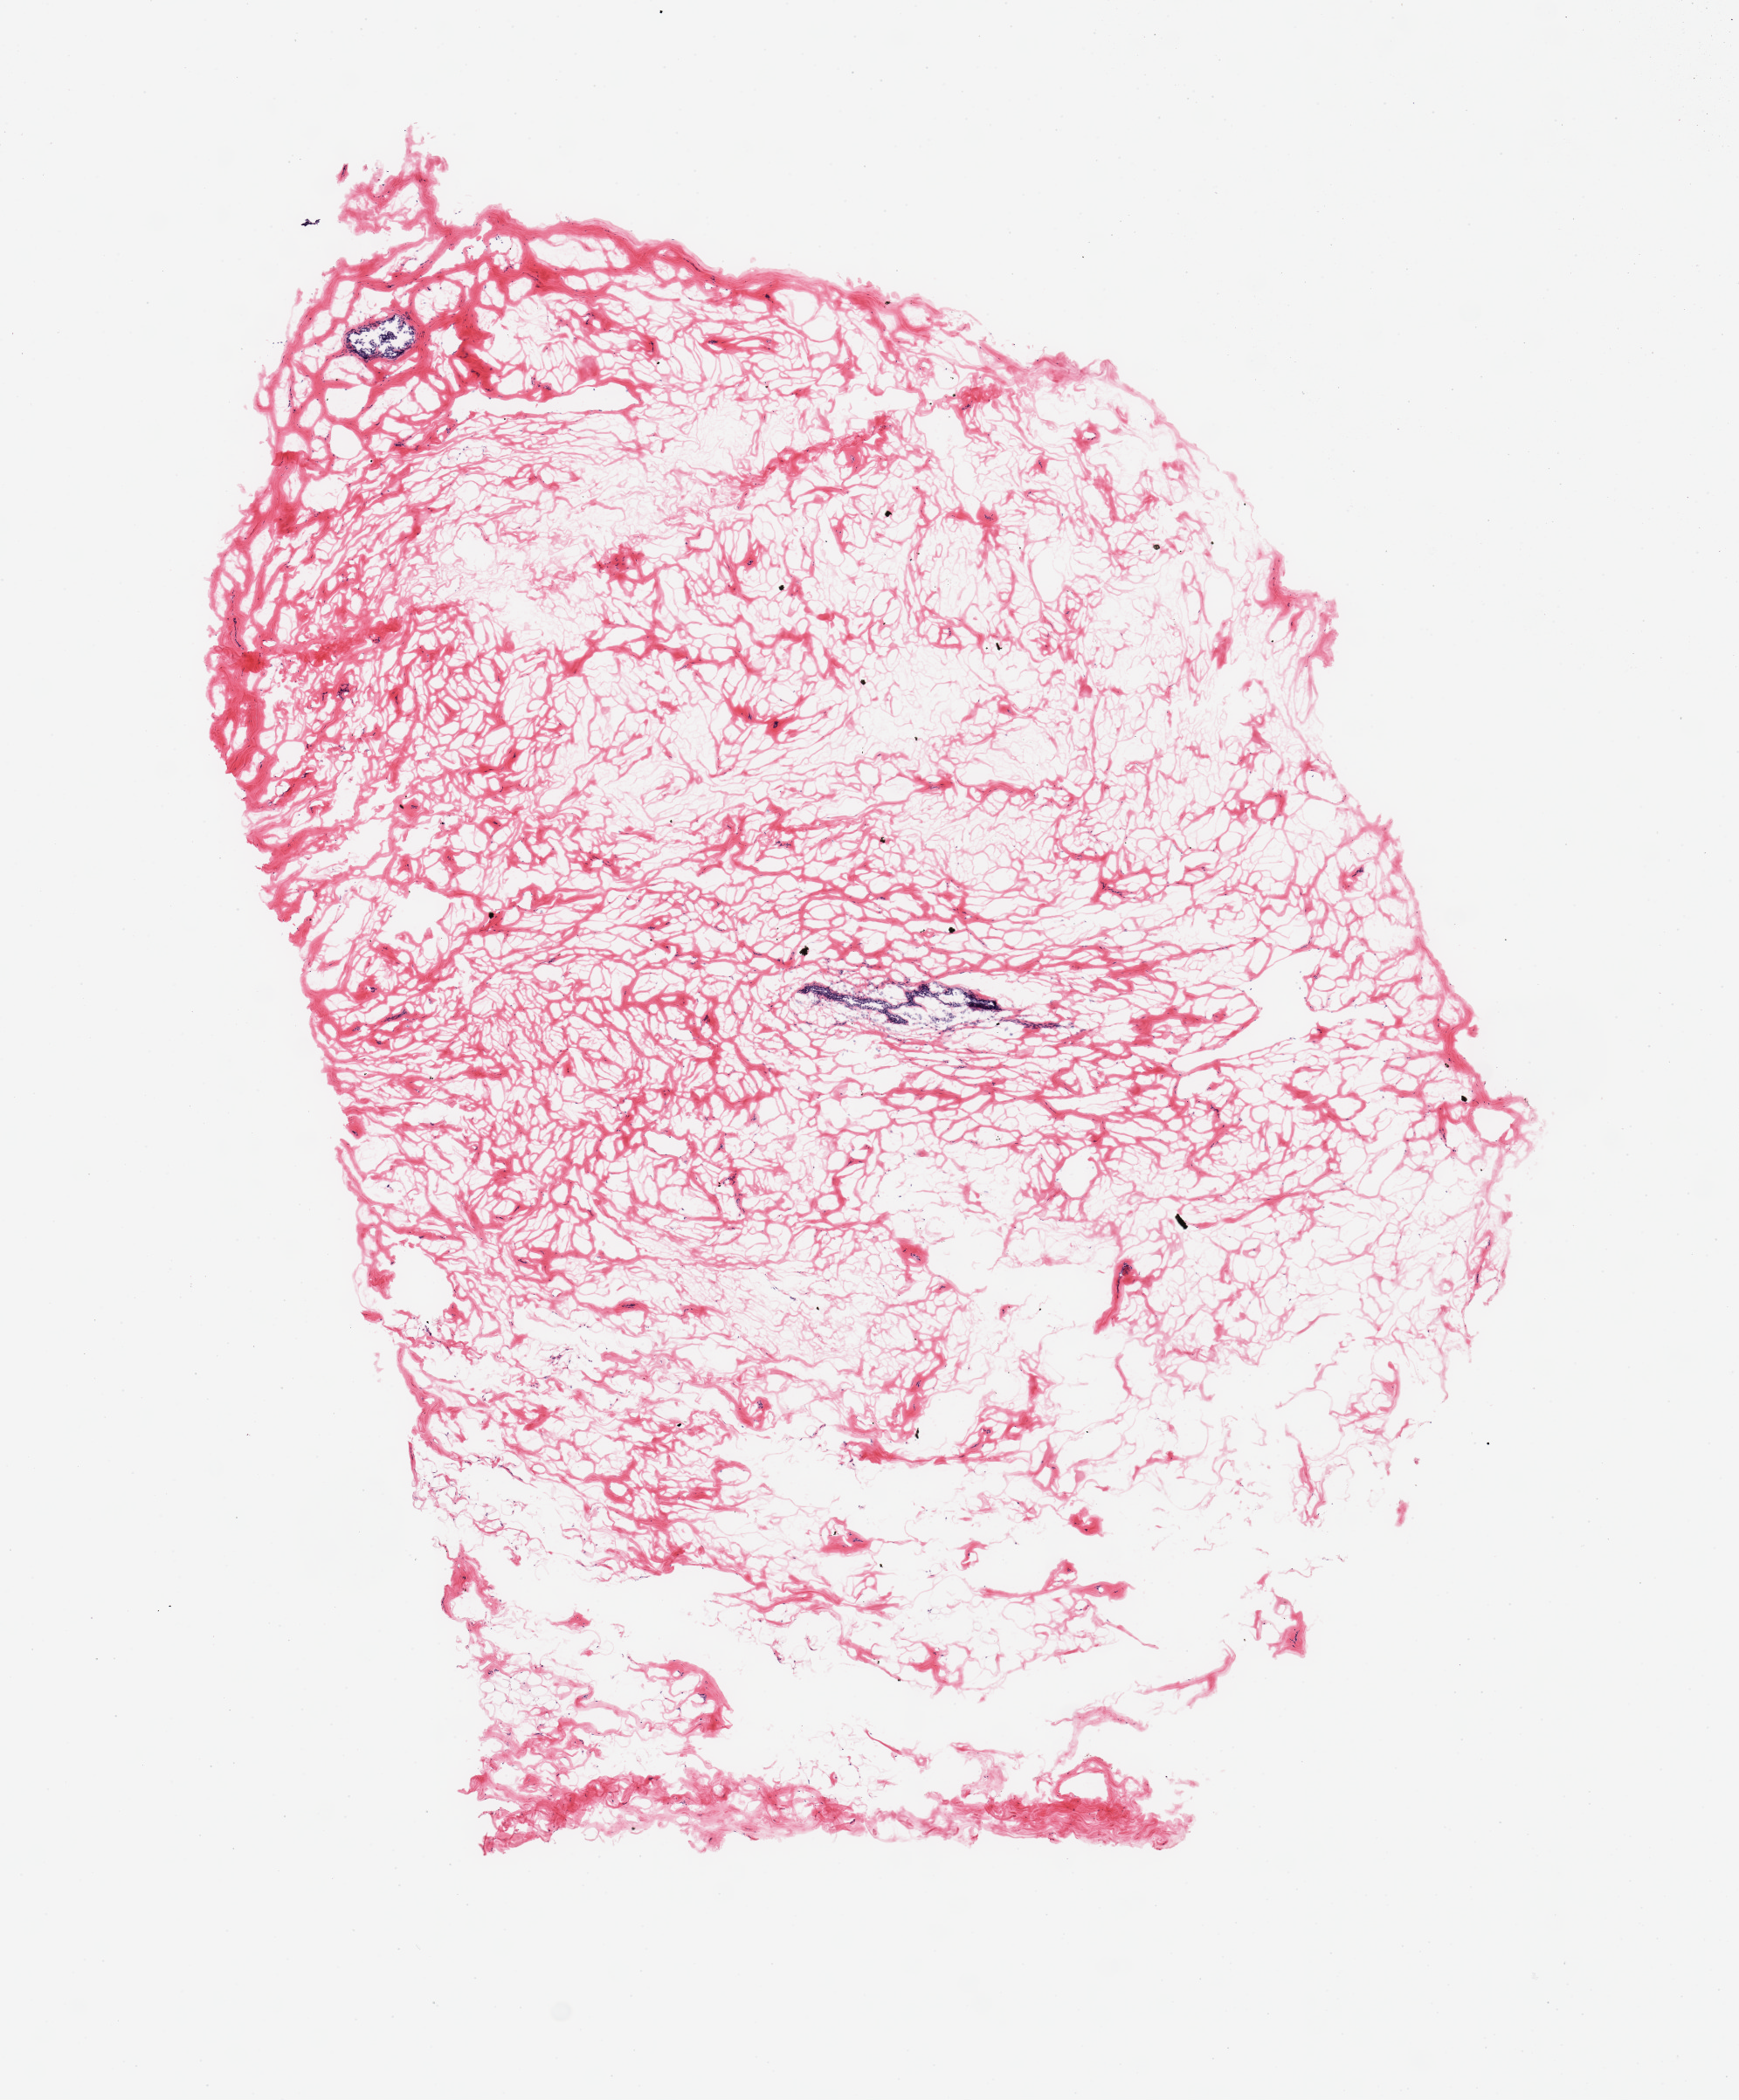
Hematoxylin and eosin (H&E) whole-slide image, low-resolution overview of the scanned area, about 7.9 x 9.5 mm (slide scanned at 20x). Frozen section. Sampled site (target tissue): breast. Donor tissue sample.
Reviewer comment on this tissue sample: 1 piece; comparable to content in PAXgene sample.